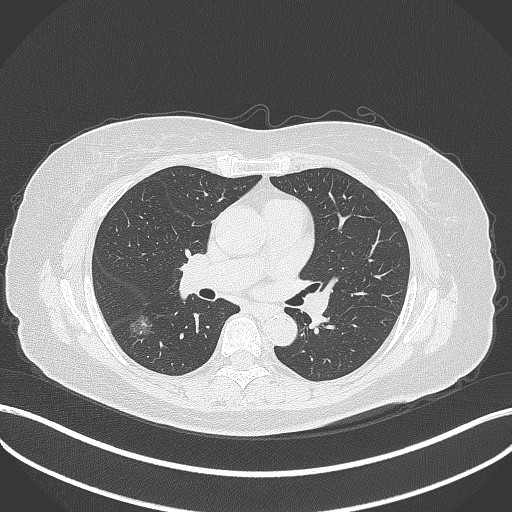
Chest CT, one axial slice; slice 175 of 322 in the series (ordered by position); reconstruction kernel B70f; lung window (W 1500 / L -600 HU); 512 × 512 image matrix. Patient: female, 64 years. From the clinical record (not read from this slice): clinical TNM (as recorded): T1c N0 M0; histopathological grade: G1.
Structures marked on this image (bounding box drawn by a radiologist):
- lung tumour (recorded histology: adenocarcinoma): bounding box (x1, y1, x2, y2) in pixels: (127, 311, 156, 338)